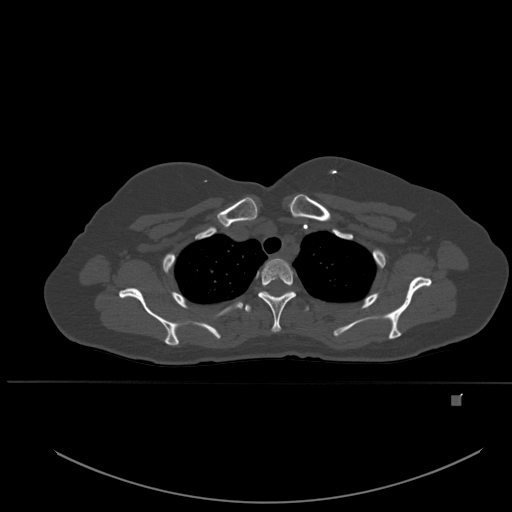
CT including the spine, one axial slice; slice 404 of 651 in the series (ordered by position); bone window (W 1800 / L 400 HU); 512 × 512 image matrix, field of view 443 × 443 mm. Patient: female, 49 years. From the clinical record (not read from this slice): primary cancer: breast.
Annotated regions visible in this slice (semi-automatic segmentation, software-assisted and operator-edited):
- T1 vertebra: box from (x=285, y=261) to (x=289, y=266) px
- T2 vertebra: (x=258, y=259)–(x=296, y=332)
- T3 vertebra: (x=245, y=291)–(x=309, y=313)